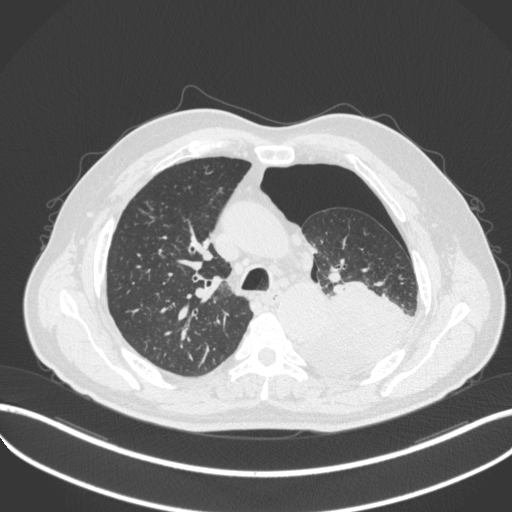
Chest CT, one axial slice; position 356 of 466 along the scan axis; 120 kVp; lung window (W 1500 / L -600 HU); 1 mm slice thickness; 512 × 512 image matrix. Patient: male, 76 years. From the clinical record (not read from this slice): clinical TNM (as recorded): T3 N0 M1b.
Annotated regions visible in this slice (rectangle marked by the reading radiologist):
- lung tumour (recorded histology: adenocarcinoma): bounding box <287,282,418,381> (left, top, right, bottom; pixels)